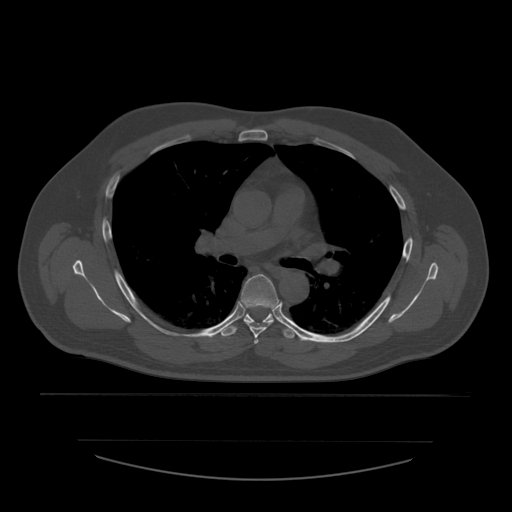
CT including the spine, one axial slice; position 390 of 532 along the scan axis; 120 kVp; bone window (W 1800 / L 400 HU); 512 × 512 image matrix, field of view 441 × 441 mm. Patient age 44 years. Case-level facts recorded for this patient, not image findings: primary cancer: soft tissue sarcoma.
Structures marked on this image (semi-automatically segmented with operator editing):
- T4 vertebra: bounding box (x1, y1, x2, y2) in pixels: (254, 338, 259, 344)
- T5 vertebra: (241, 274, 279, 338)
- T6 vertebra: (220, 313, 297, 339)